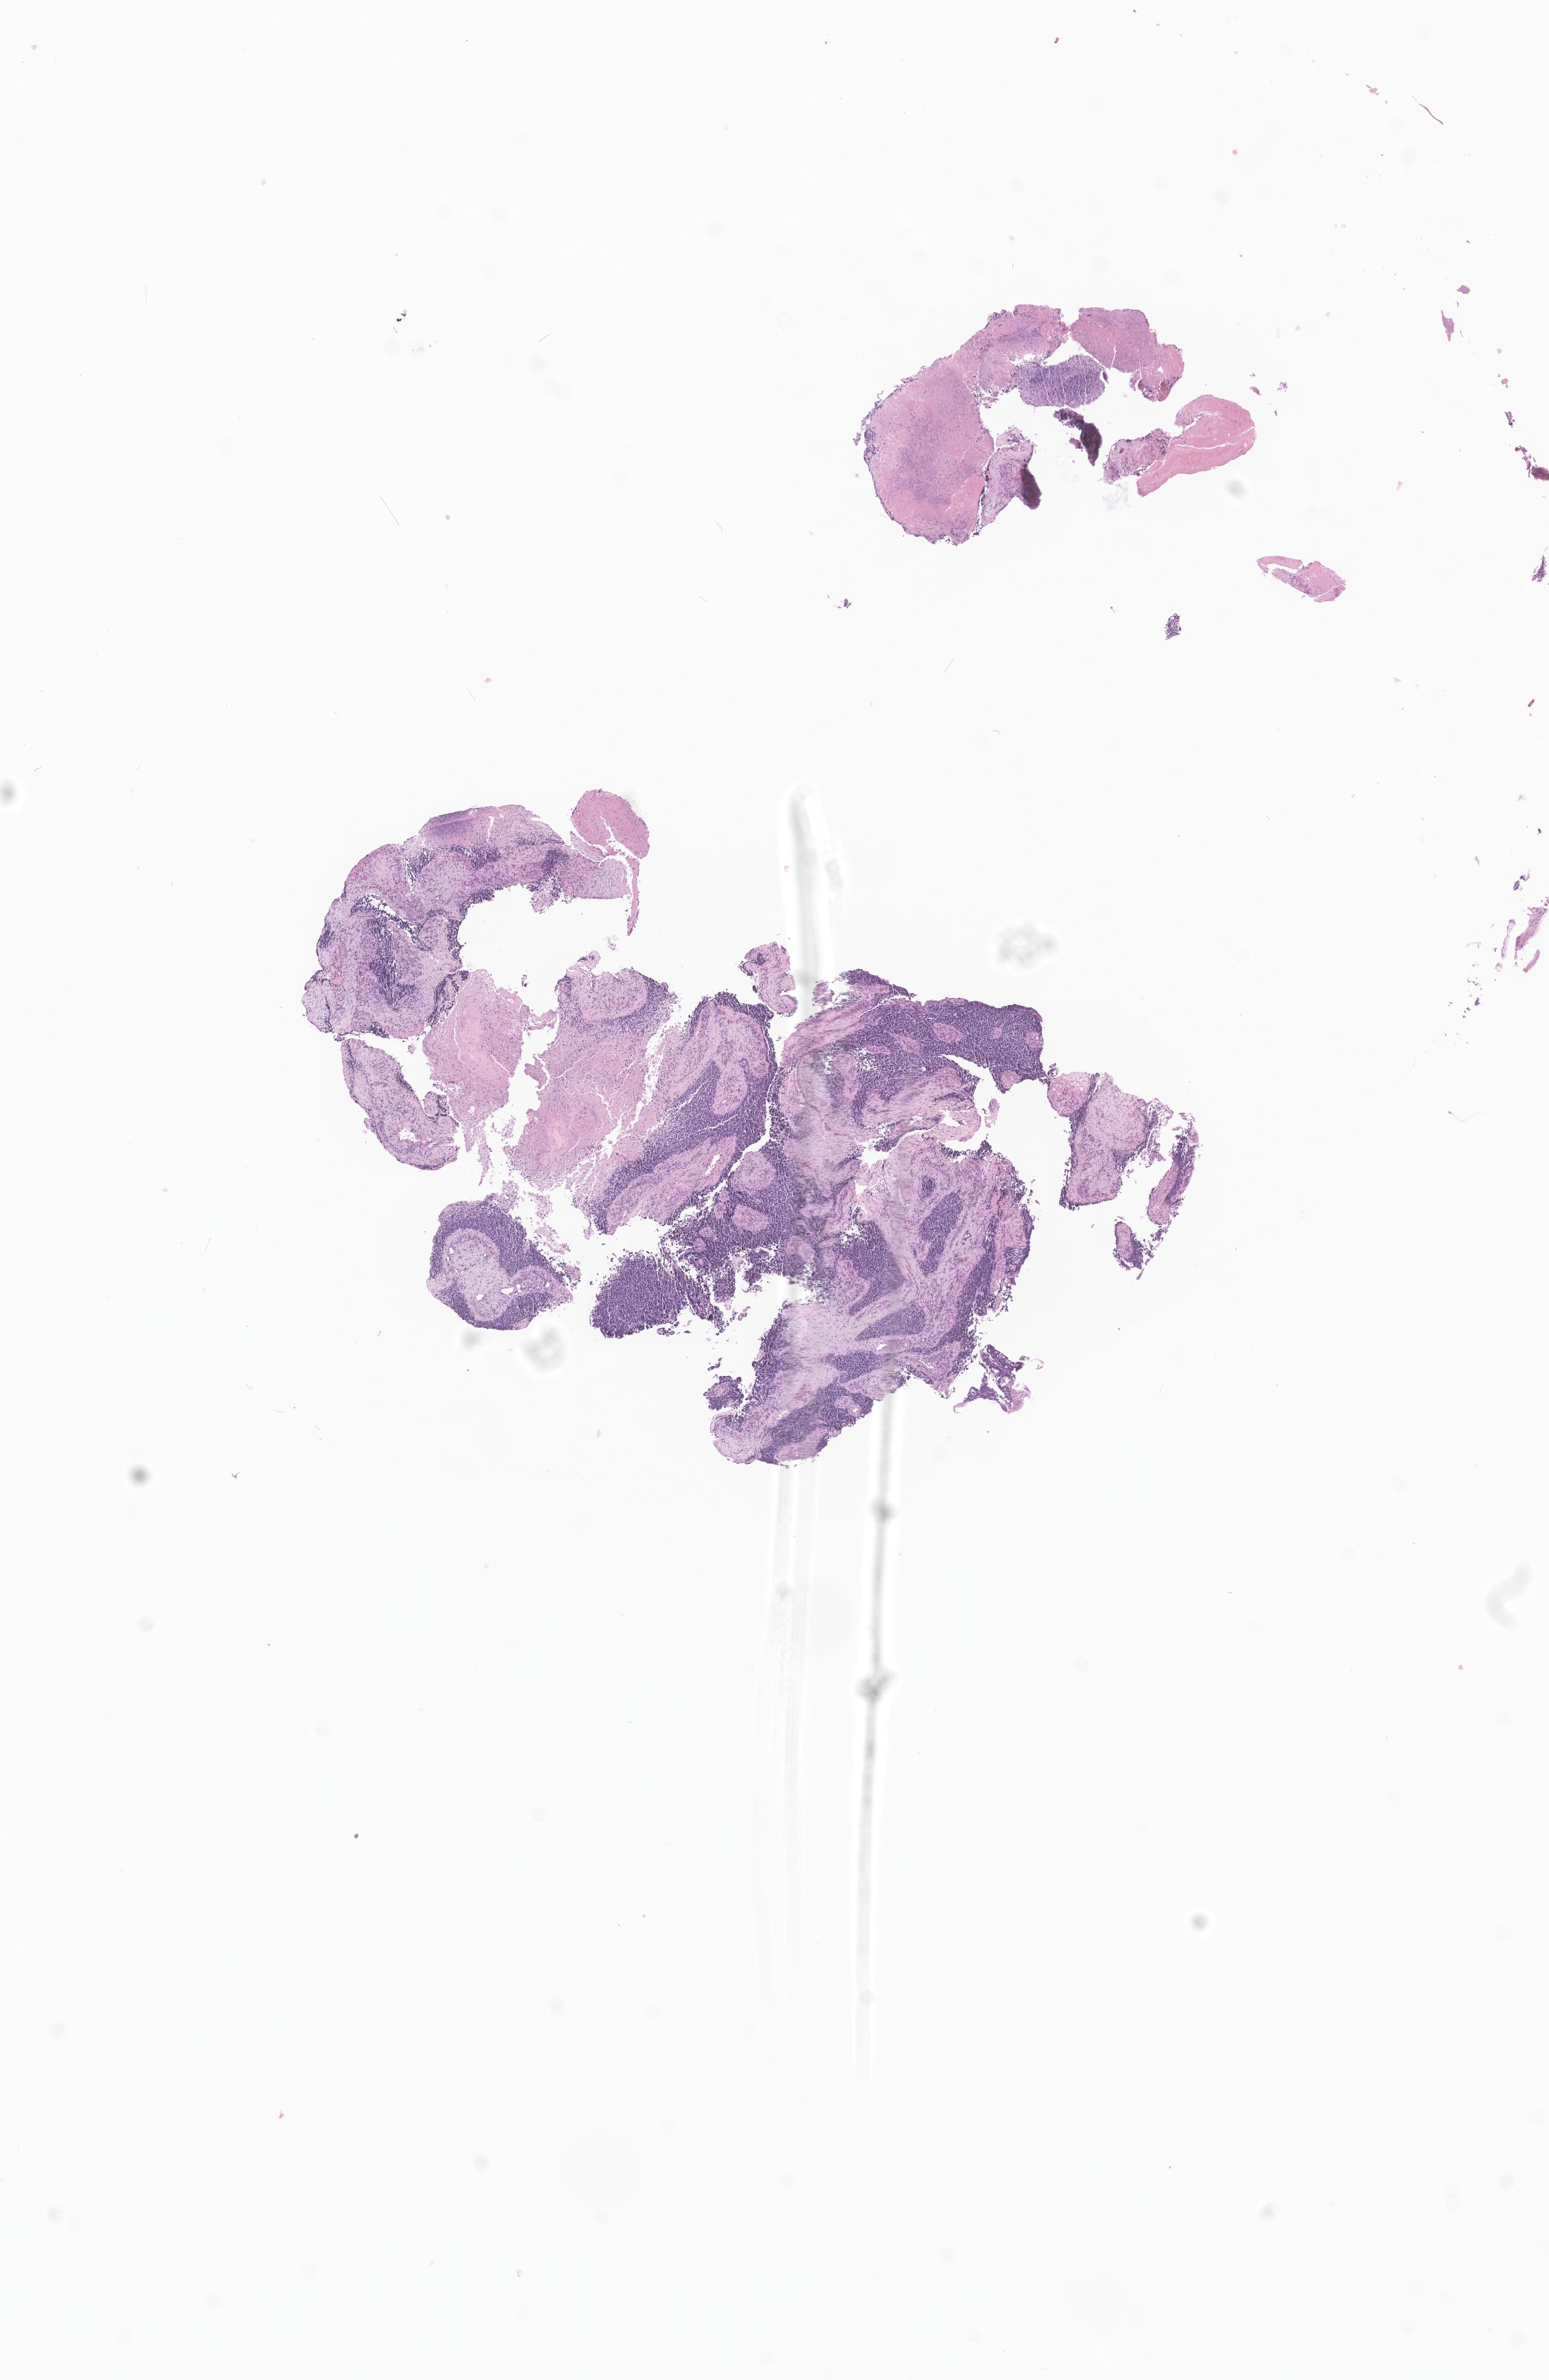
Digitized hematoxylin and eosin (H&E)-stained section of tumor tissue from the nasopharynx — a low-resolution overview of the entire scanned area, about 9.5 x 14.6 mm; formalin-fixed, paraffin-embedded (FFPE) tissue. Patient: female, age 44 months (3 years 8 months).
* diagnosis: Rhabdomyosarcoma, NOS